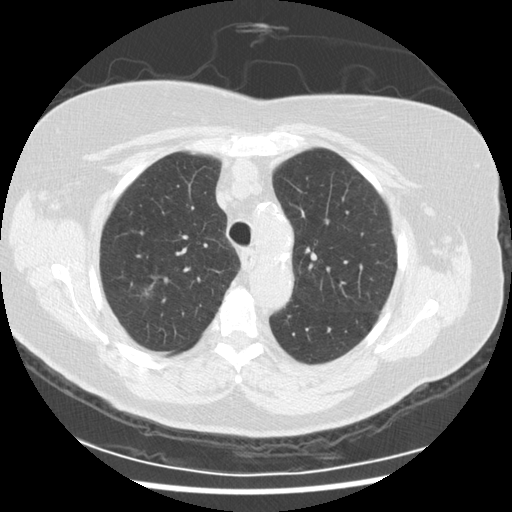
Chest CT (low-dose screening protocol), one axial image, third annual screen, lung window (W 1500 / L -600 HU), 2.5 mm slice thickness, standard (soft-tissue) reconstruction kernel (STANDARD), 120 kVp, 512 × 512 image matrix. Female participant, aged 72 years at enrolment. Current smoker at enrolment.
Lesion marked by an expert reader, bounding box [x1, y1, x2, y2] px = [130, 278, 165, 311]. Screening reader's record for this exam (one nodule recorded; not confirmed to be the boxed lesion): non-calcified nodule or mass ≥4 mm, right upper lobe, 9 × 8 mm, poorly defined margins, ground glass attenuation, pre-existing on the prior screen: no. Official screen result: positive, other.